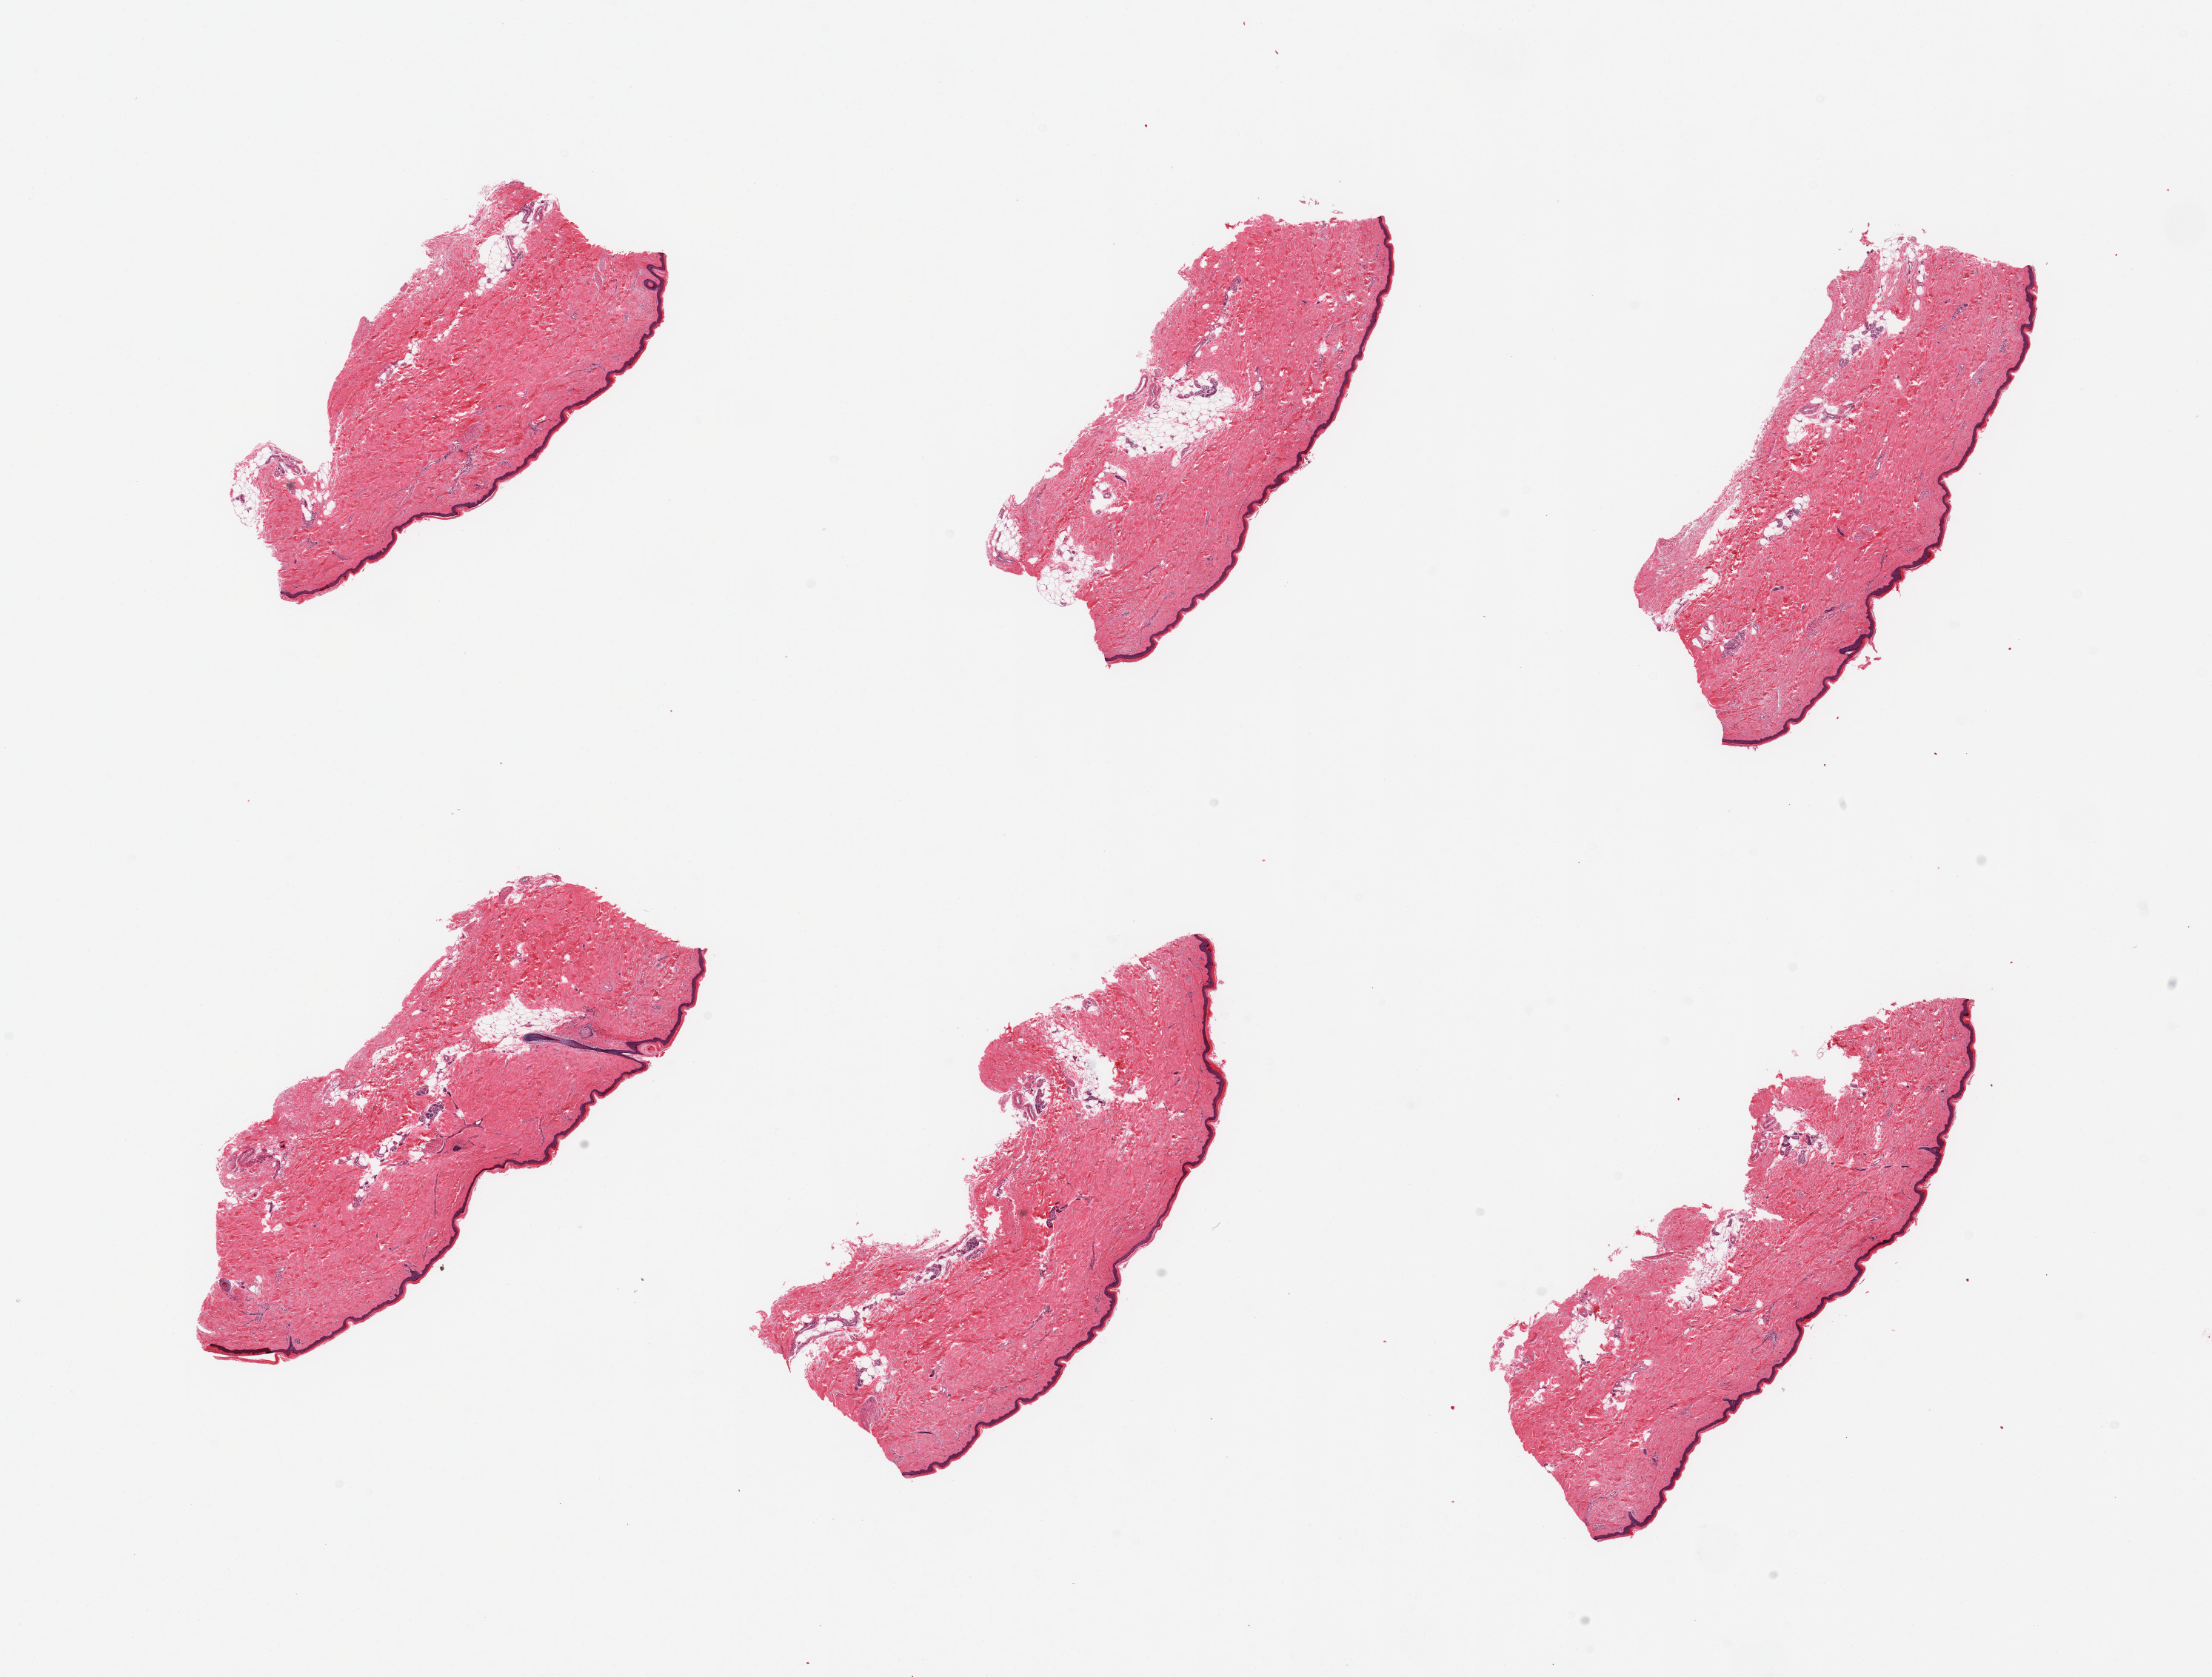
Digitized haematoxylin and eosin-stained section, whole scanned area (about 23.6 x 17.9 mm, acquisition: 20x scan) shown as a low-resolution overview, PAXgene-fixed, paraffin-embedded tissue, sampled site (target tissue): skin of lower leg, tissue donor sample. Donor: female.
Reviewer comment on this tissue sample: 6 pieces, trace dermal fat; squamous epithelium is ~40-50 microns.